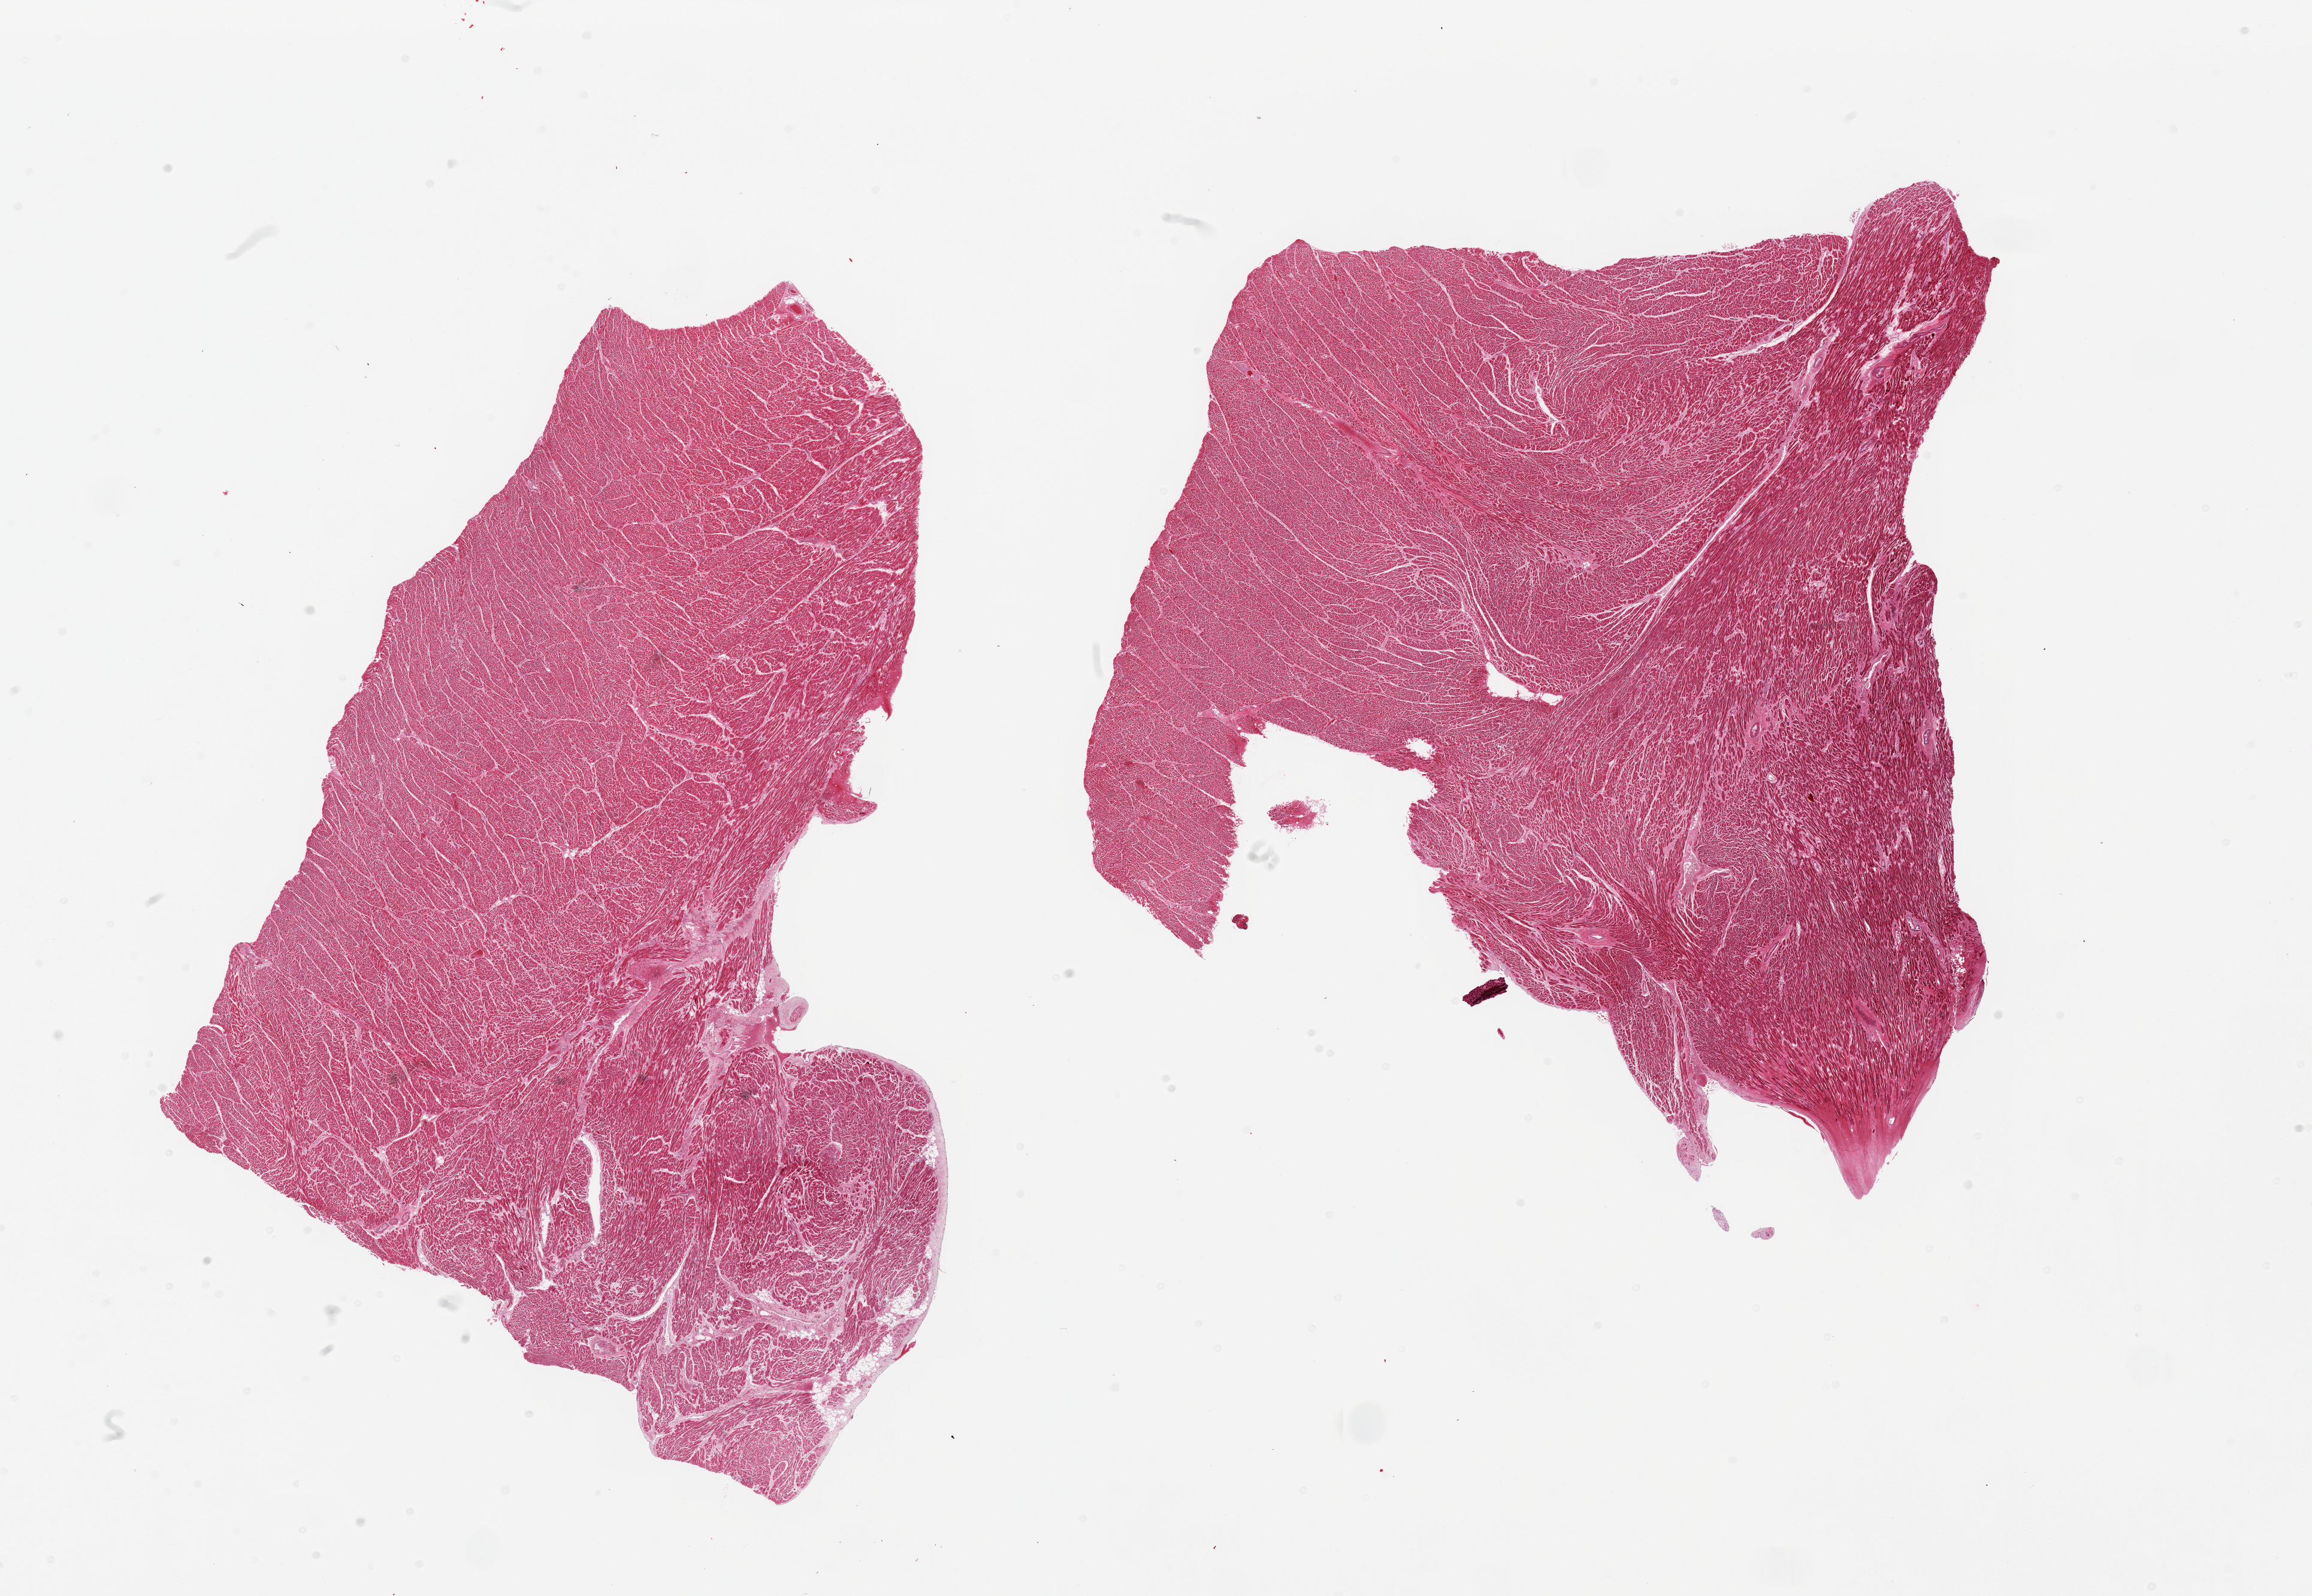
Haematoxylin and eosin whole-slide image — whole scanned area (about 30.5 x 21.1 mm, acquisition: 20x scan) shown as a low-resolution overview; PAXgene-fixed, paraffin-embedded tissue; section of heart (target tissue); tissue donor sample.
Pathologist's review note for this sample: 2 pieces, moderate interstitieal fibrosis, microinfarct (remote).